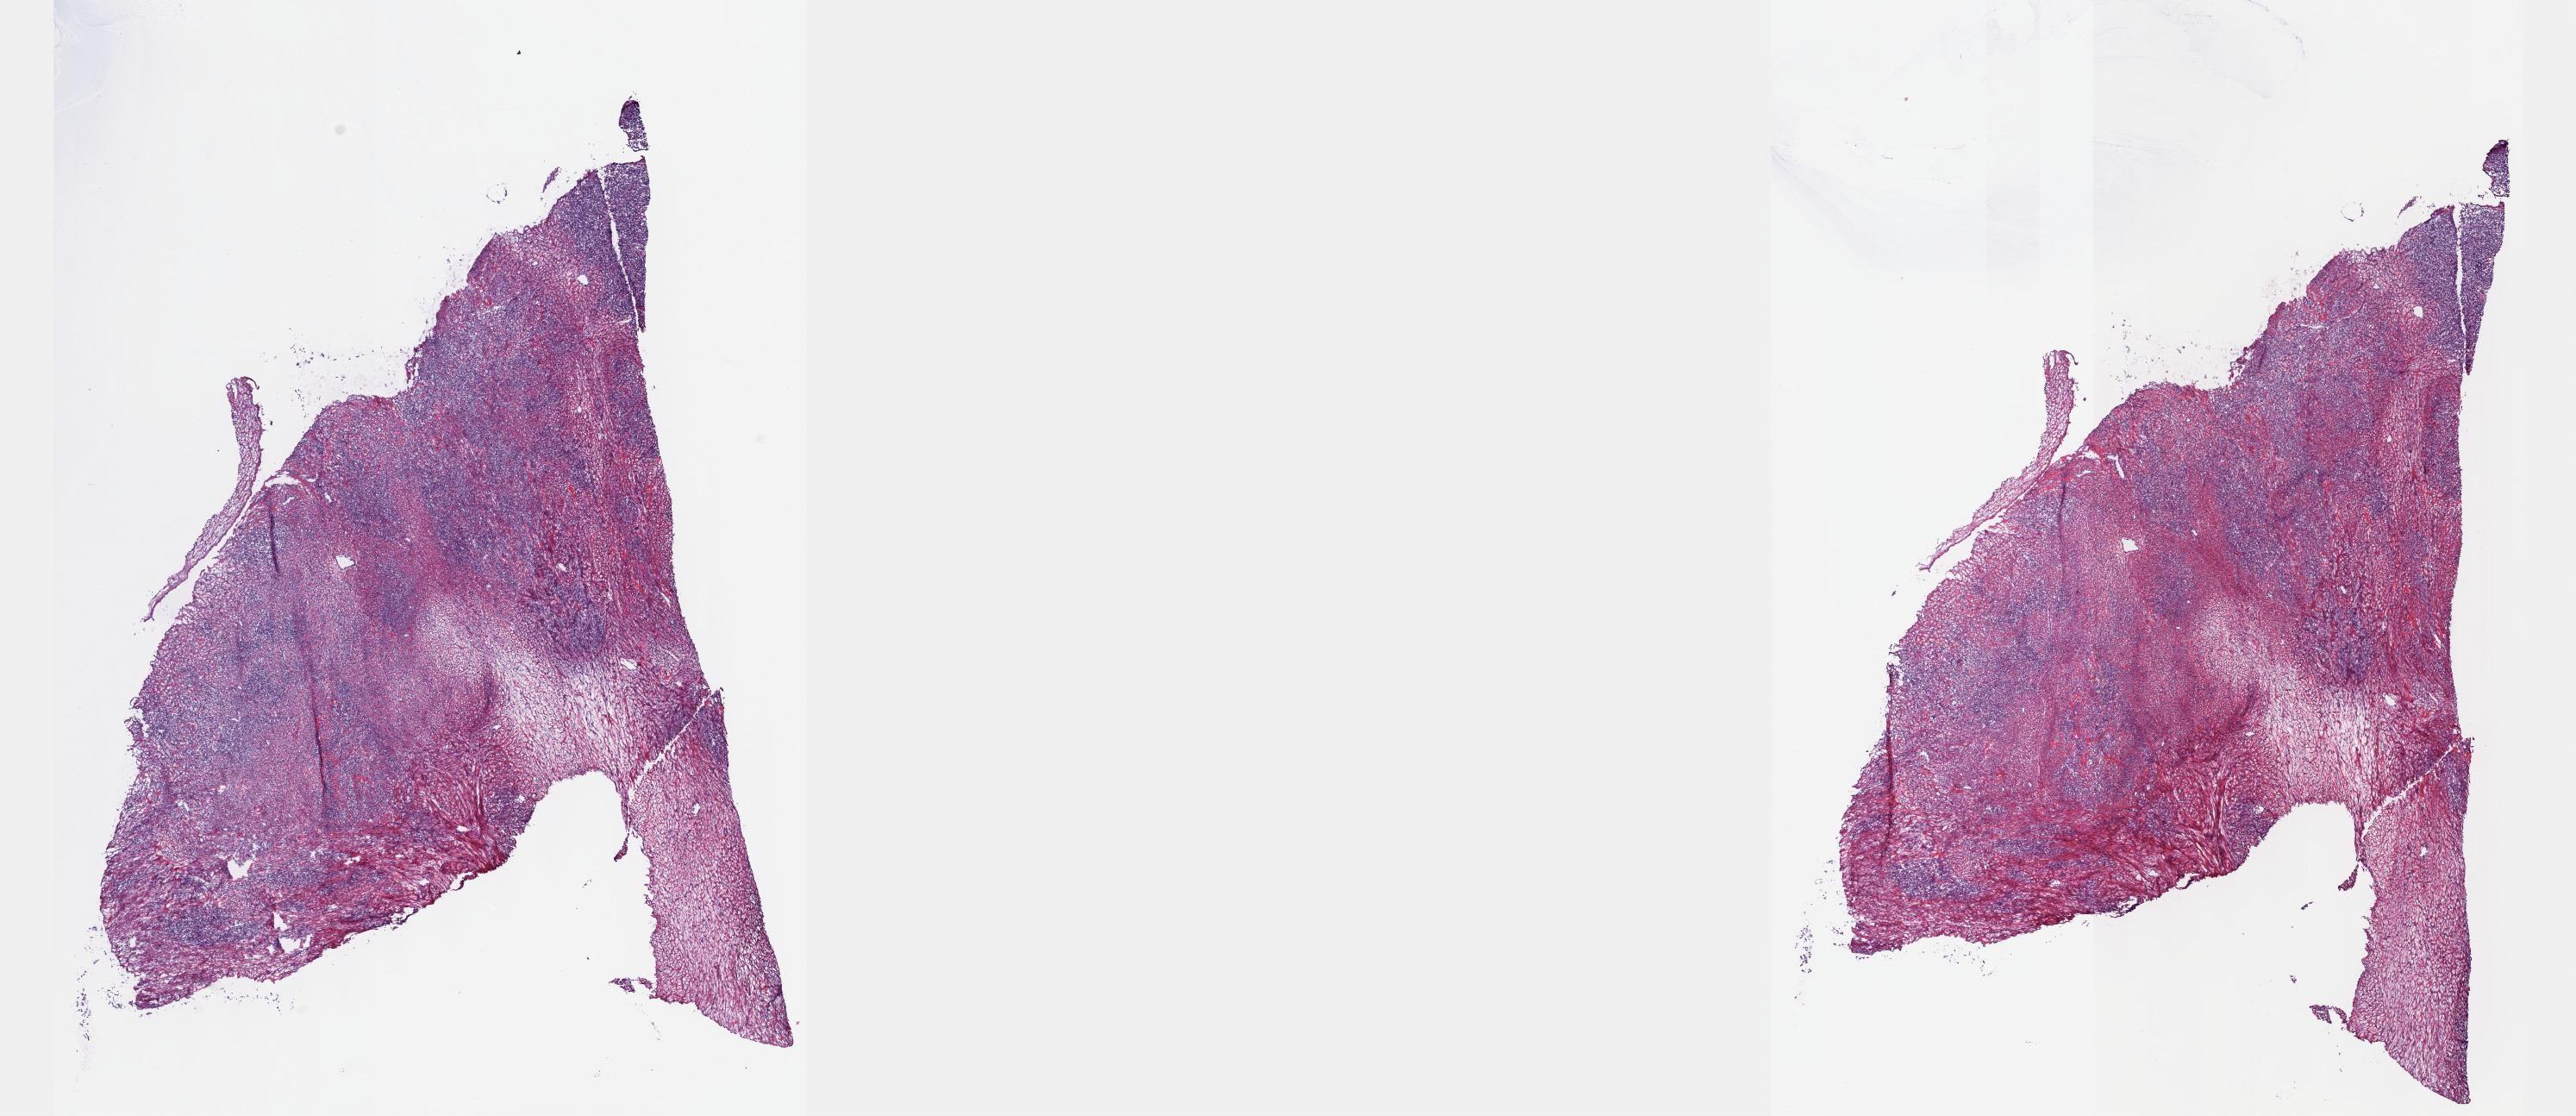
H&E whole-slide image, a low-resolution overview of the entire scanned area, about 24.1 x 10.5 mm. Frozen section. Sample: primary tumour, retroperitoneum and peritoneum. Patient: female, age at initial diagnosis 71 years.
Pathologic diagnosis: Undifferentiated sarcoma.